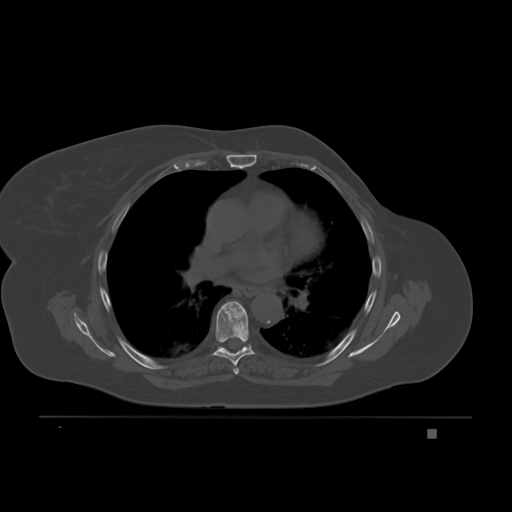
CT including the spine, one axial slice. Bone window (W 1800 / L 400 HU). 3 mm slice thickness. 512 × 512 image matrix, field of view 474 × 474 mm. Patient: female, 63 years. From the clinical record (not read from this slice): primary cancer: breast.
Annotated regions visible in this slice (semi-automatically segmented with operator editing):
- T5 vertebra: bounding box (x1, y1, x2, y2) in pixels: (233, 368, 239, 375)
- T6 vertebra: (212, 301, 256, 366)